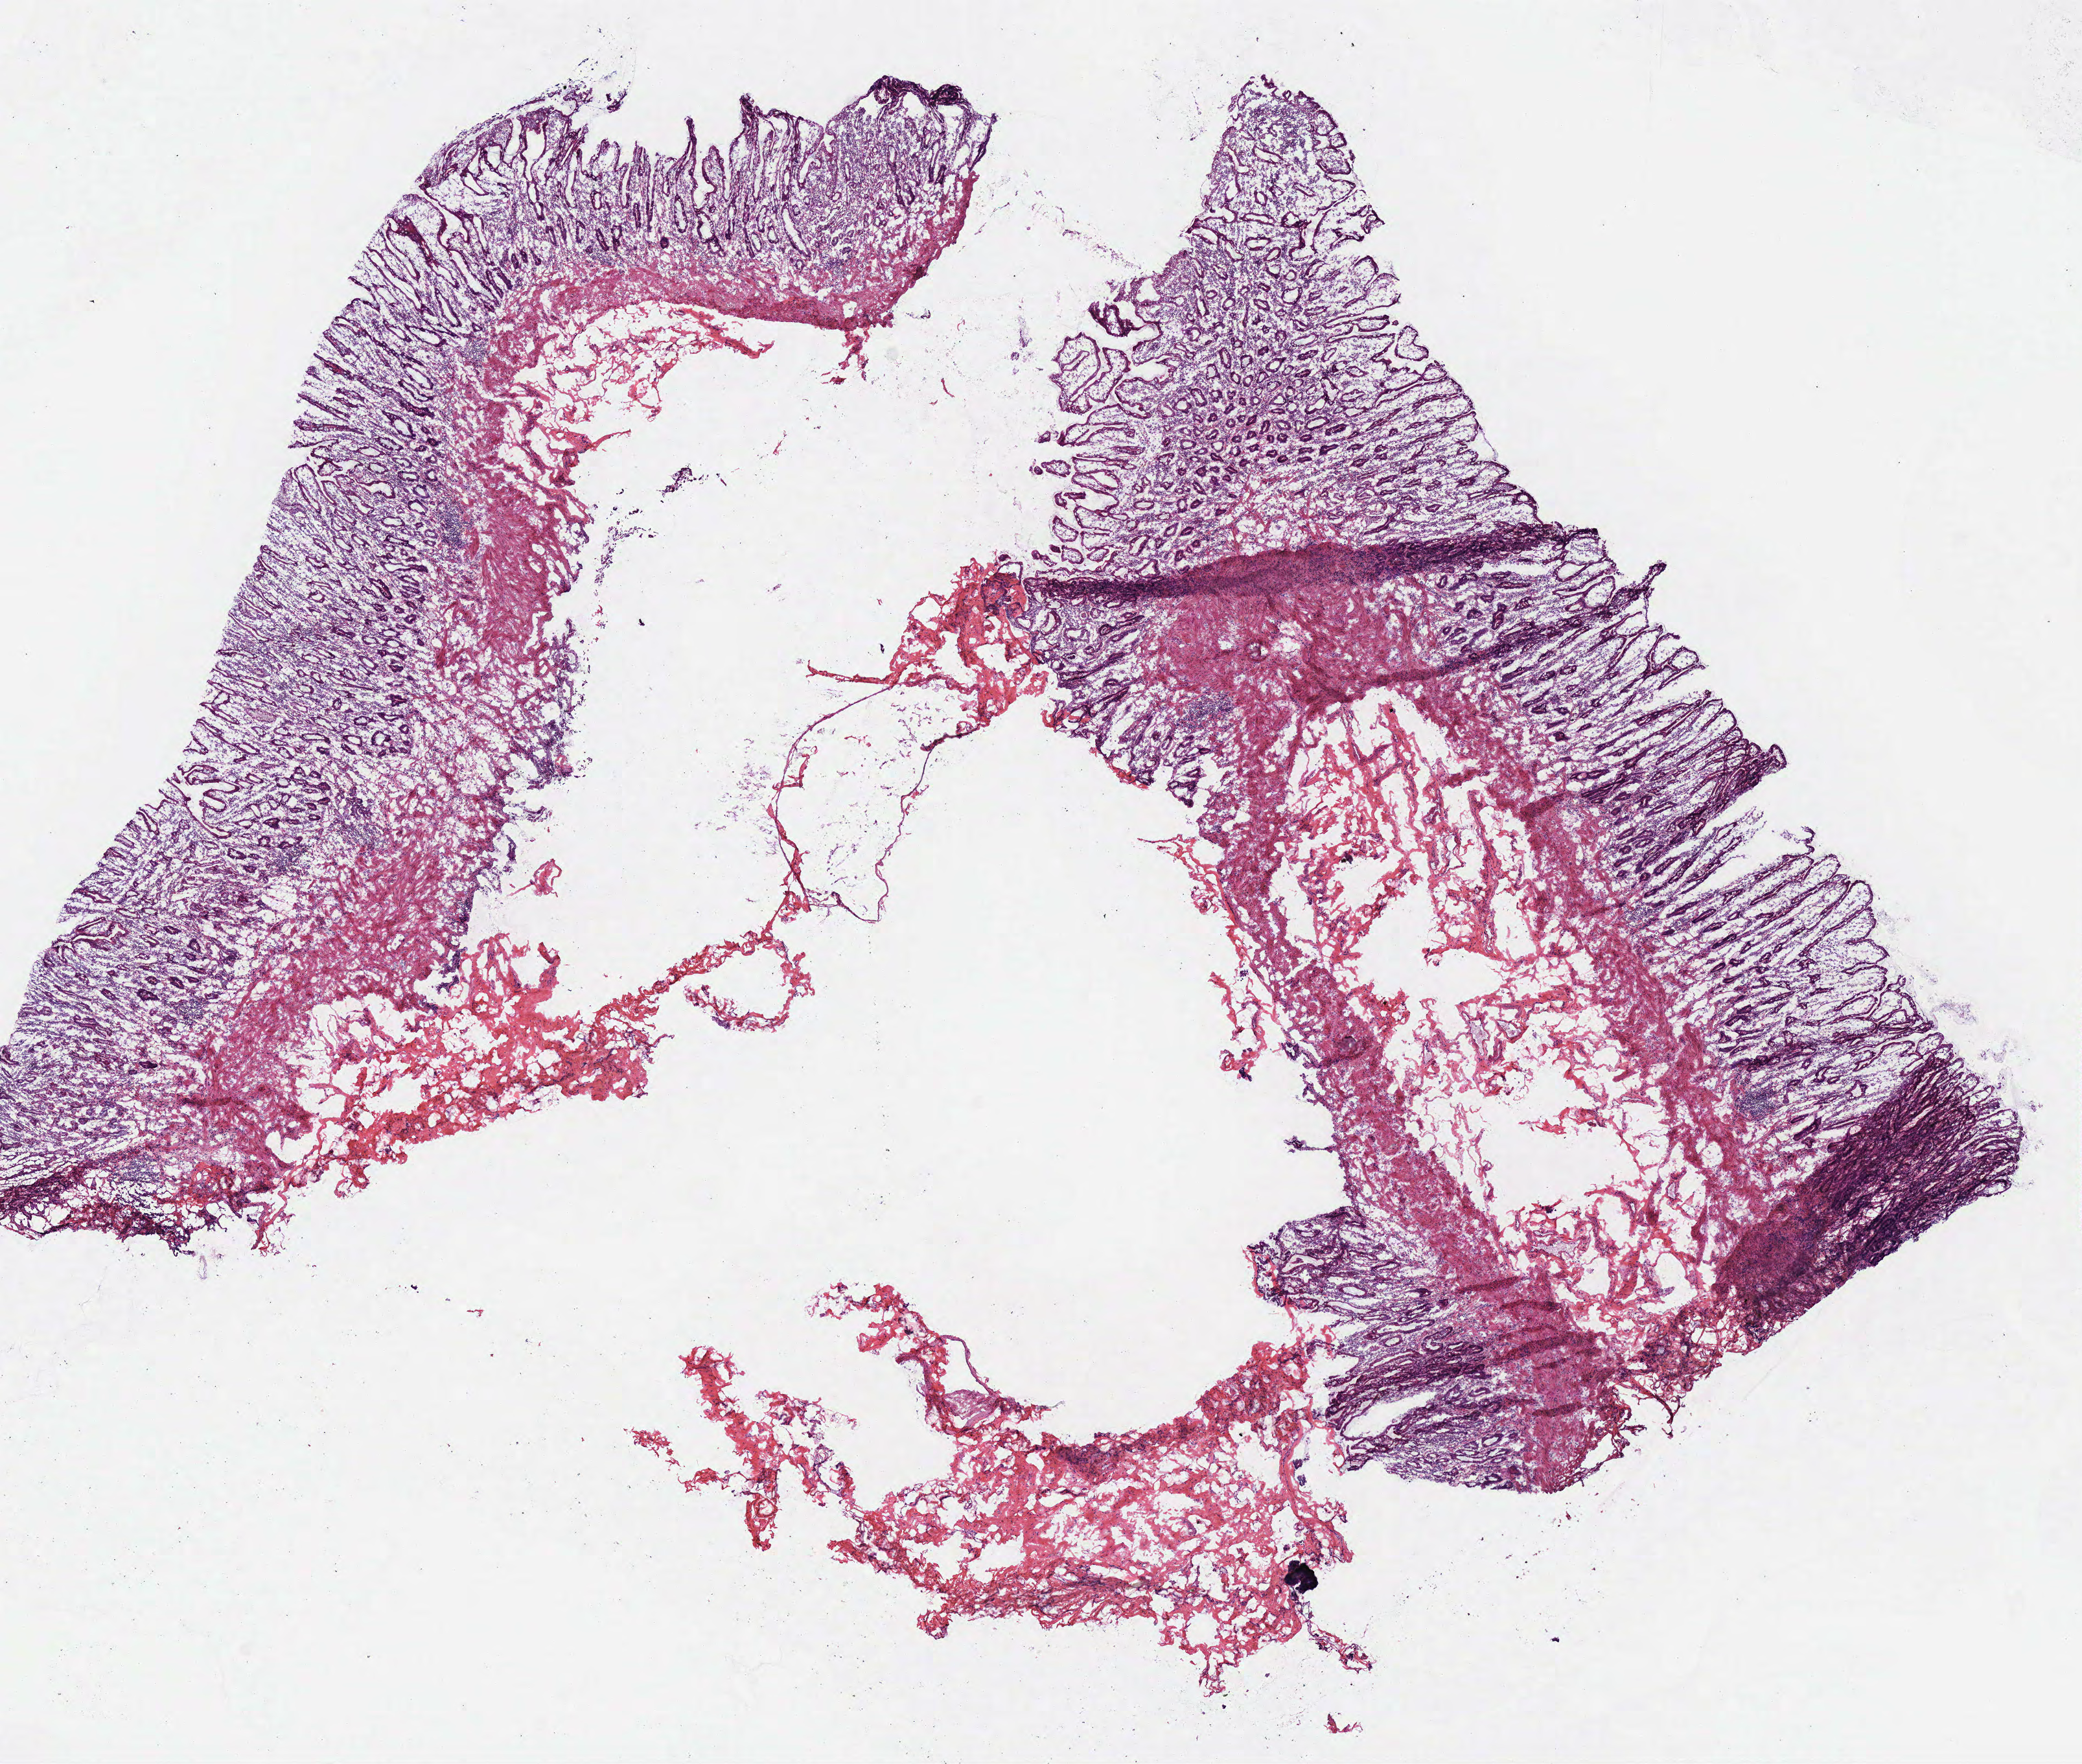
Whole-slide histology image, Hematoxylin and eosin (H&E) stained — whole scanned area (about 12.7 x 10.7 mm, from a 40x scan) shown as a low-resolution overview; frozen section from the top of the tissue portion; stomach, solid tissue normal (non-tumour tissue) sample. Male, age 69 years at initial diagnosis. Inflammatory infiltration, as recorded: lymphocyte infiltration 40%, neutrophil infiltration 12%.
• this section: solid tissue normal (non-tumour) sample from the same patient
• patient diagnosis: Adenocarcinoma, NOS